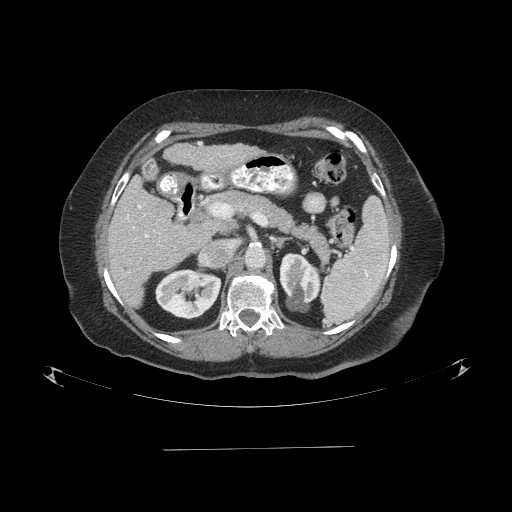
Contrast-enhanced abdominal CT (liver protocol), one axial slice; position 44 of 103 along the scan axis; reconstruction kernel STANDARD; 120 kVp; one of 2 acquisitions stored at this slice position; soft-tissue window (W 400 / L 40 HU); 512 × 512 image matrix, field of view 500 × 500 mm. Case-level facts recorded for this patient, not image findings: diagnosis: hepatocellular carcinoma (patient treated with transarterial chemoembolisation; whether this scan precedes or follows treatment is not stated here); TNM stage (as recorded): Stage-IIIA; Child-Pugh class: A; tumour nodularity: multinodular.
Annotated regions visible in this slice (semi-automatically segmented with operator editing):
- liver parenchyma outside the tumour (the mass and vessels are separate outlines, so this box may not span the whole liver): bounding box <108,176,212,306> (left, top, right, bottom; pixels)
- liver vessels: <127,205,149,238>